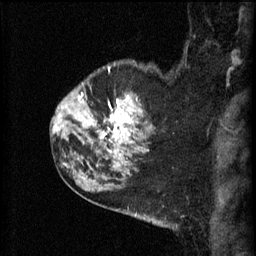
Breast MRI (dynamic contrast-enhanced), one sagittal slice; position 48 of 60 along the scan axis; 3 images stored at this slice position (order not interpretable as contrast timing); 1.5 T; TE 4.2 ms, TR 11 ms; 2.3 mm slice thickness; 256 × 256 image matrix, field of view 180 × 180 mm. Patient: female, 52 years.
Structures marked on this image (semi-automatic segmentation, software-assisted and operator-edited):
- analysis volume of interest (the breast-tissue region the enhancement analysis was run in; not a lesion): bounding box (x1, y1, x2, y2) in pixels: (86, 78, 155, 157)
- tumour enhancement mask (voxels above the 70 % enhancement threshold inside the analysis volume of interest): (100, 96, 141, 147)